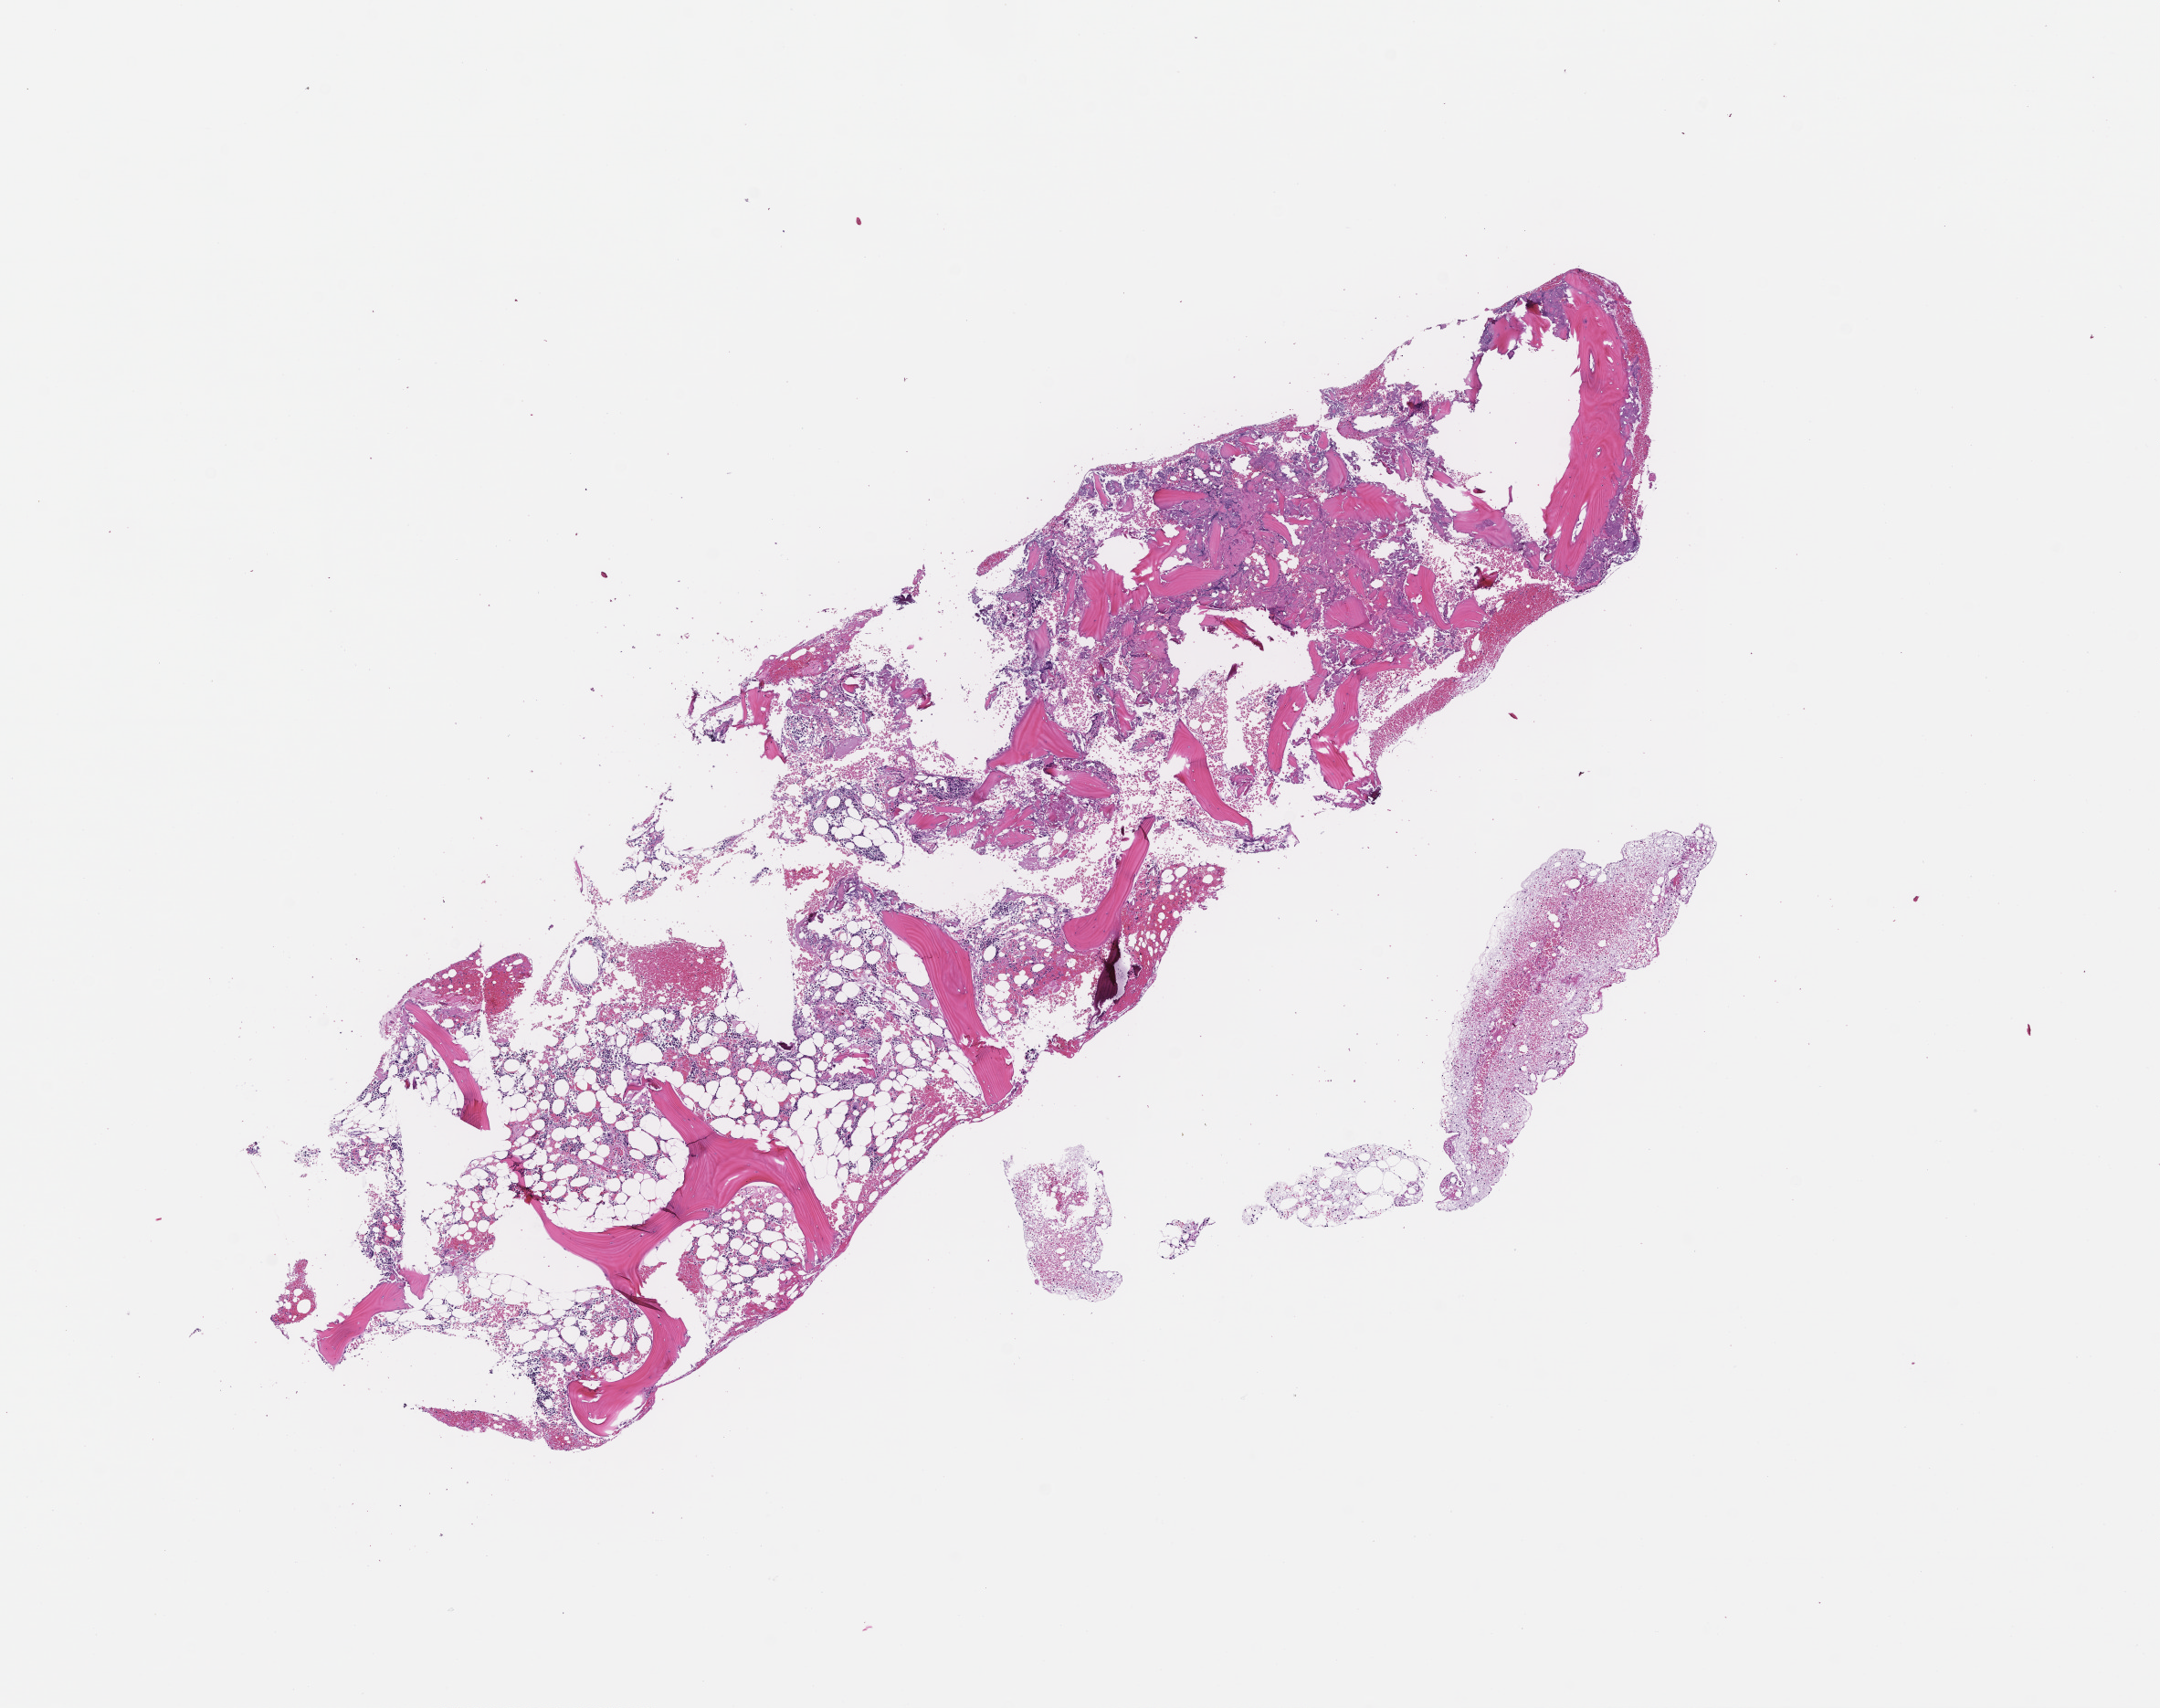
H&E whole-slide image, low-resolution overview of the scanned area, about 9.5 x 7.6 mm; formalin-fixed paraffin-embedded section; tissue site: bone marrow. Patient sex: male.
Patient diagnosis: Plasma Cell Myeloma.